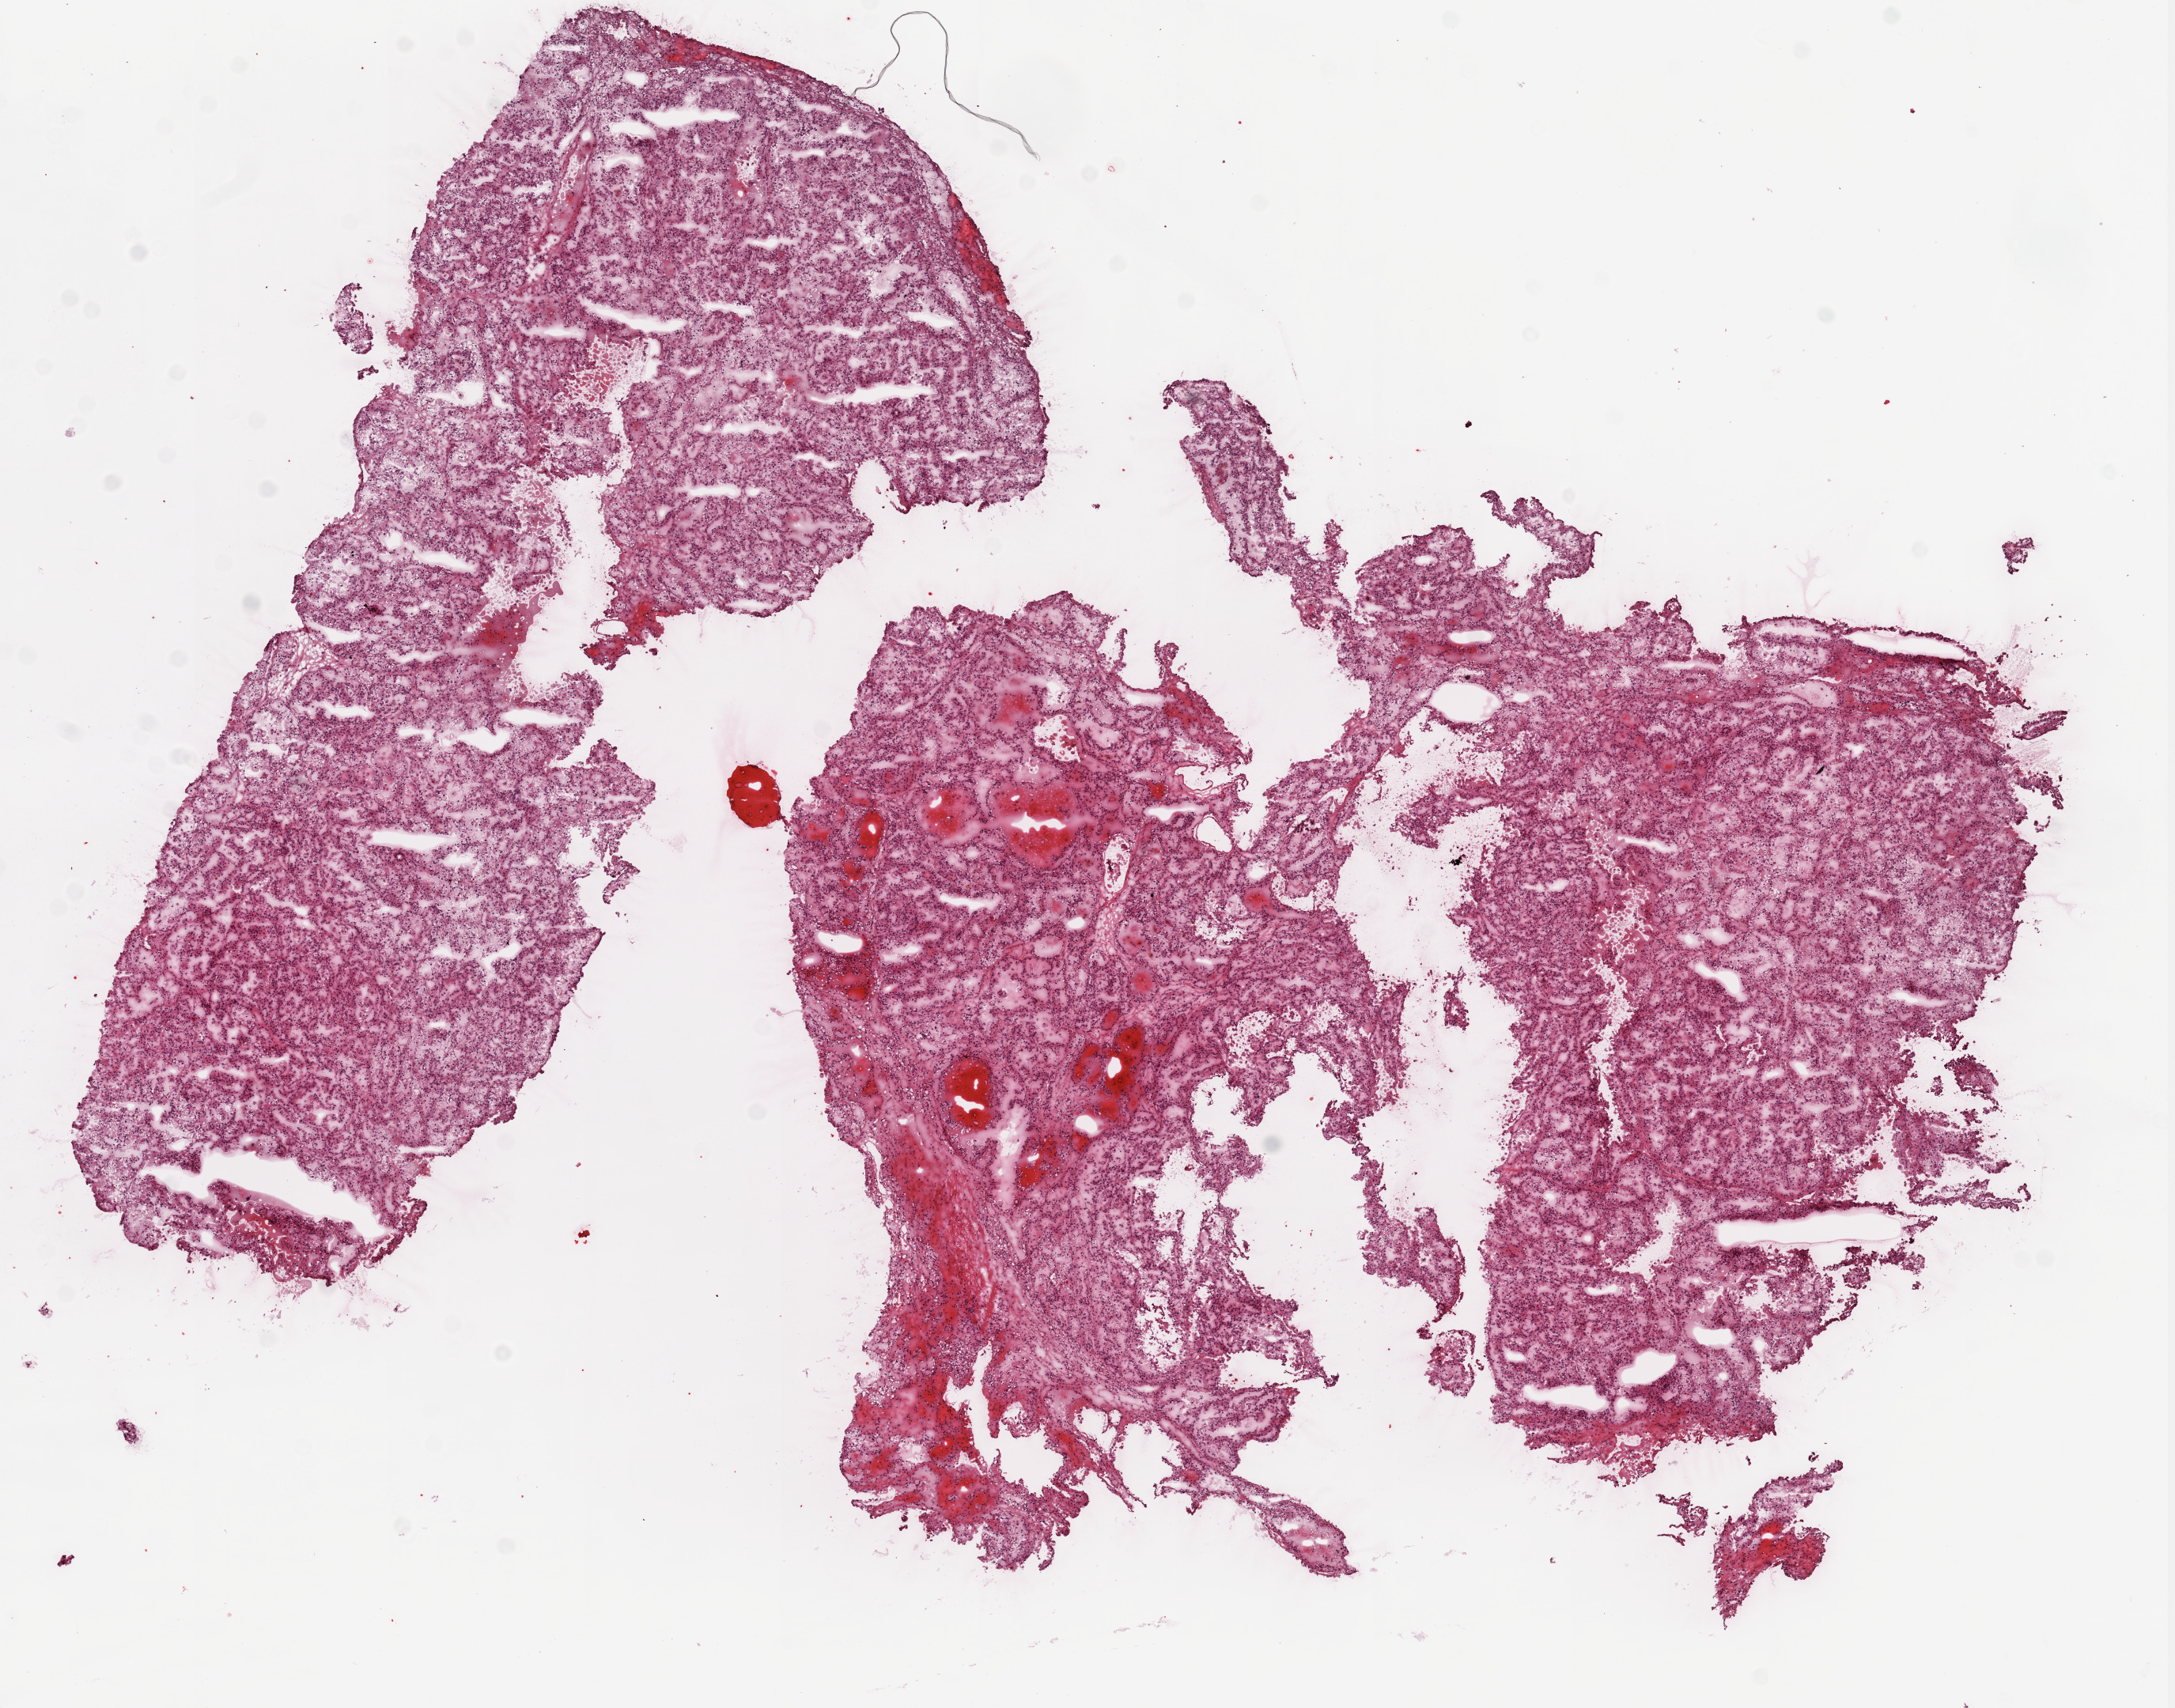
Hematoxylin and eosin (H&E) stained whole-slide image — a low-resolution overview of the entire scanned area, about 11.0 x 8.7 mm (acquisition: 20x scan); frozen section from the top of the tissue portion; primary tumour sample from the kidney. Female, age 45 years at initial diagnosis. Histologic grade: G2 (moderately differentiated). Pathologist review of this section (percent, as recorded): tumour cells 95%, tumour nuclei 85%, normal cells 0%, stromal cells 5%, necrosis 0%.
Diagnosis: Clear cell adenocarcinoma, NOS. AJCC pathologic stage: I. Laterality: left.